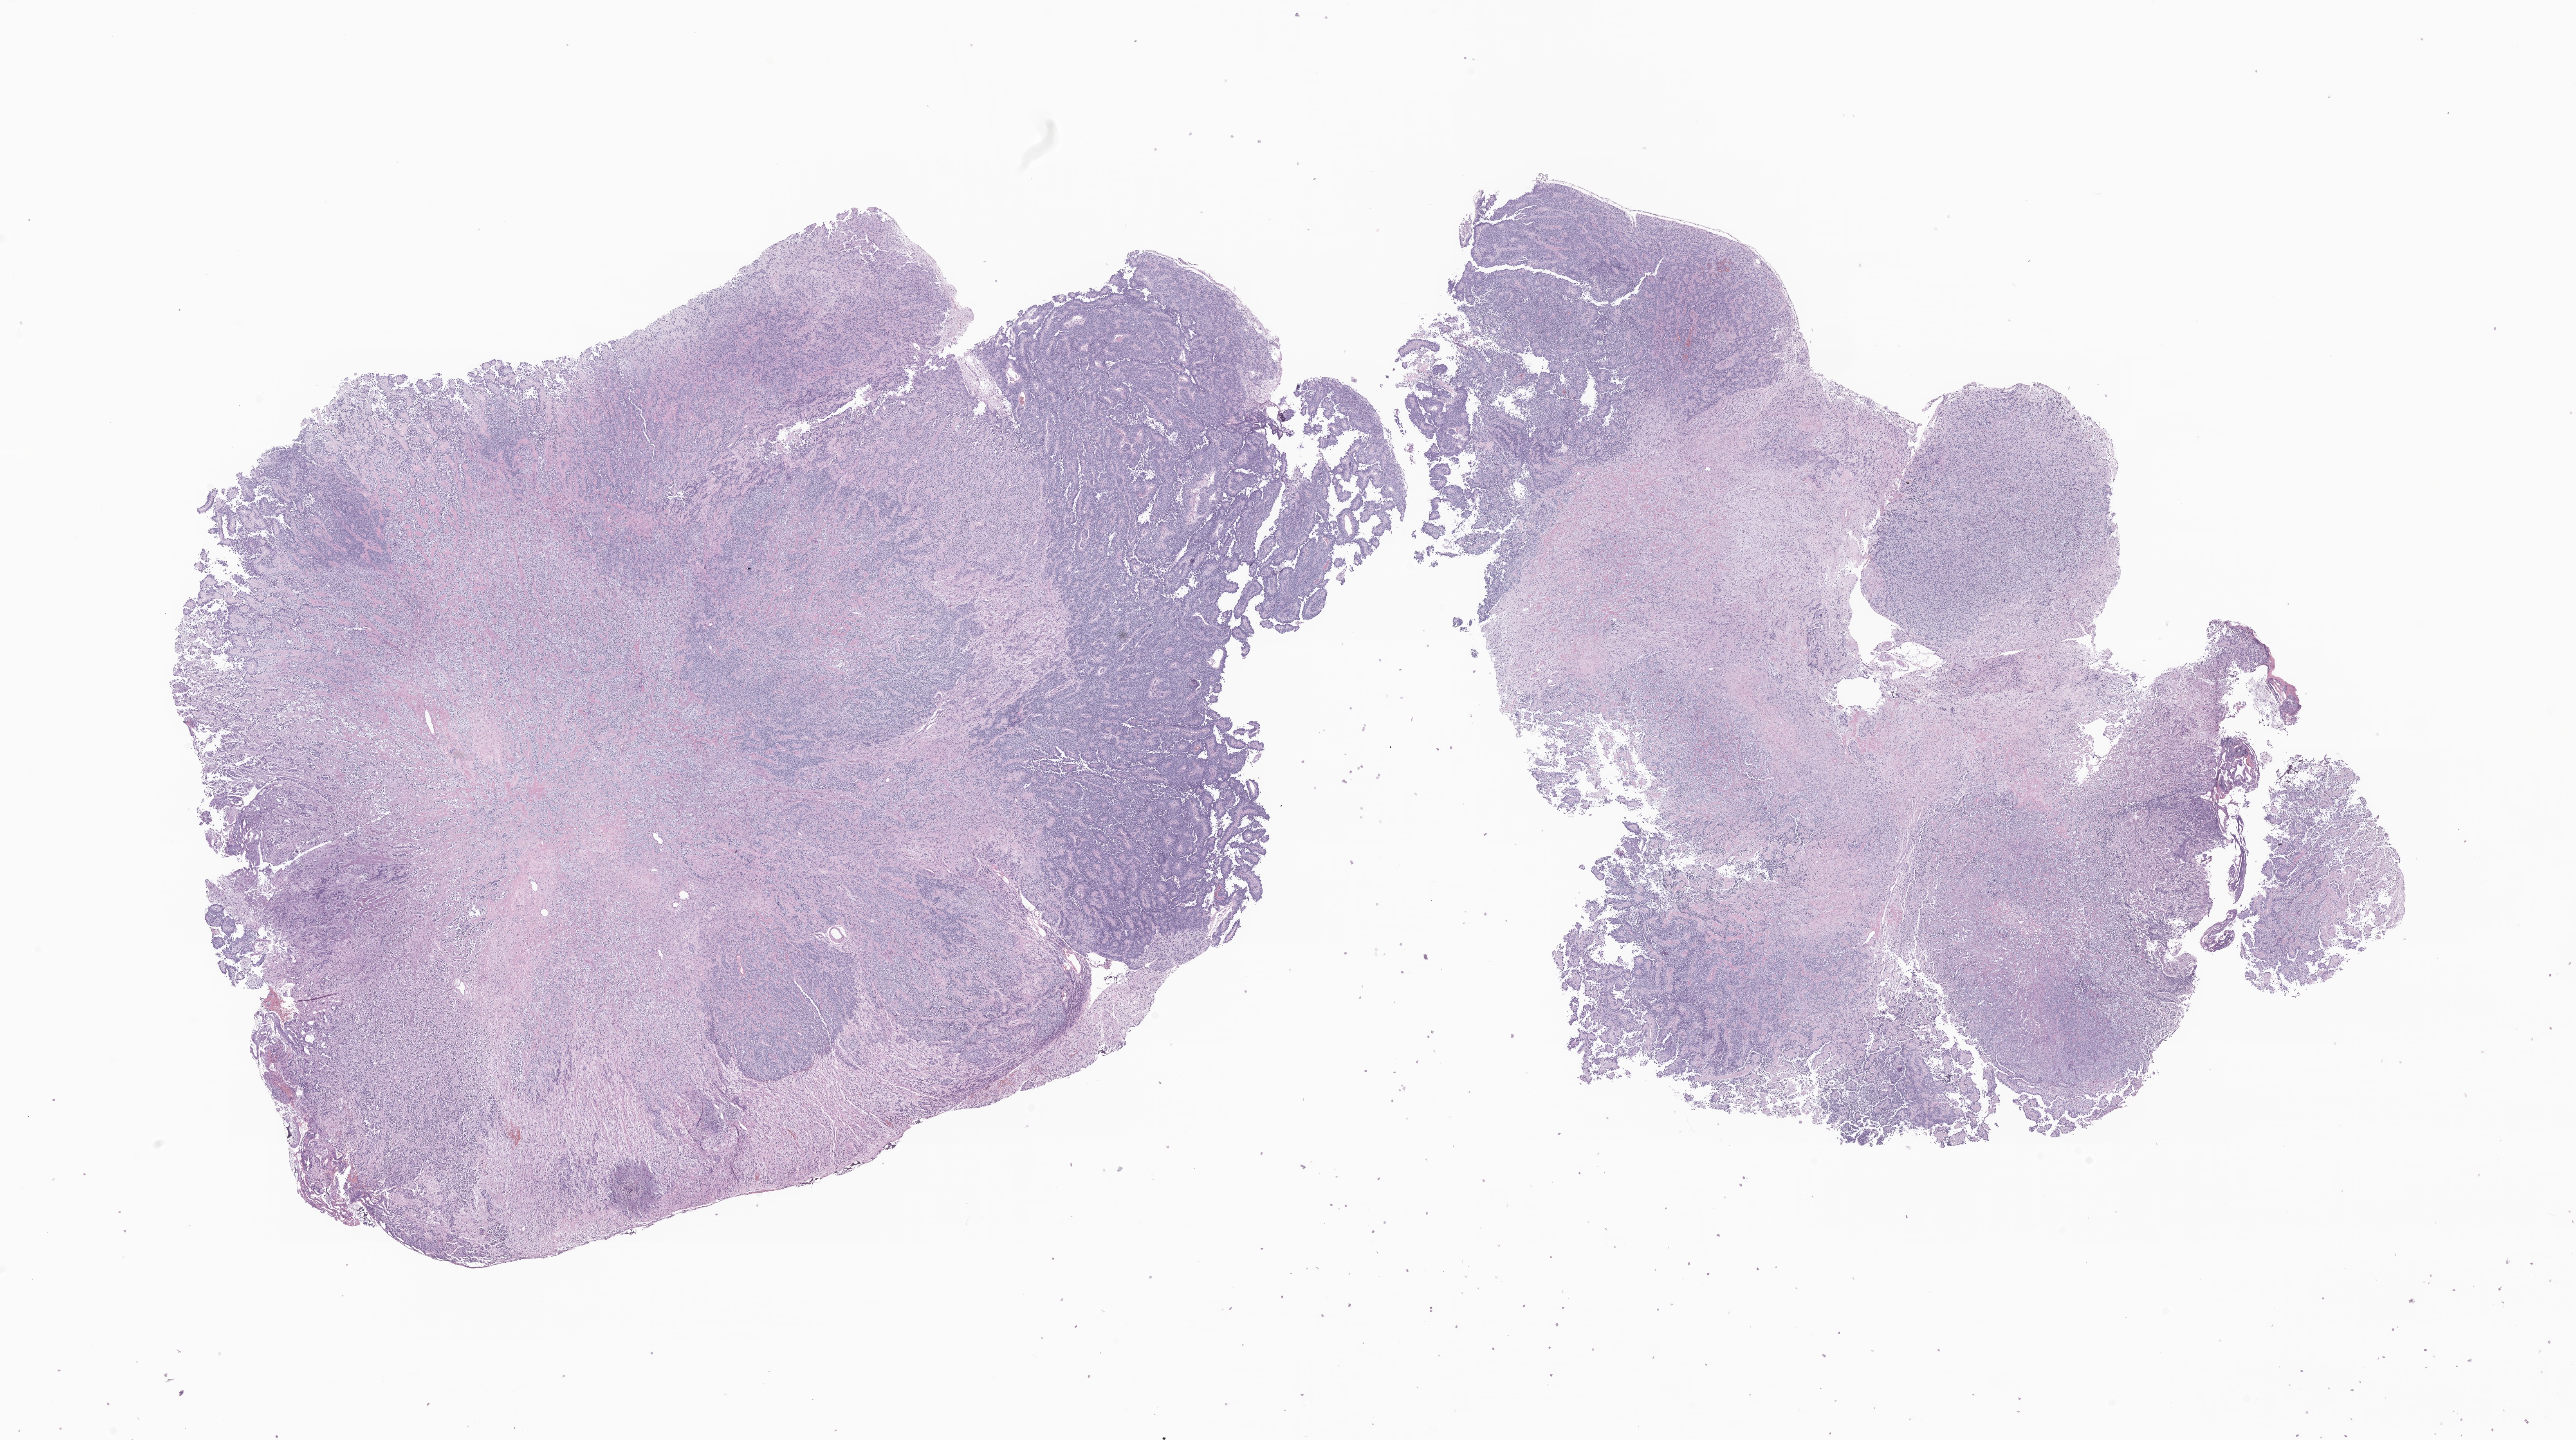
H&E whole-slide image of tumor tissue from the occipital lobe, a low-resolution overview of the entire scanned area, about 27.7 x 15.5 mm; FFPE section. Female patient, age 106 months.
Diagnosis (ICD-O-3 morphology term): Neuroepithelioma, NOS.